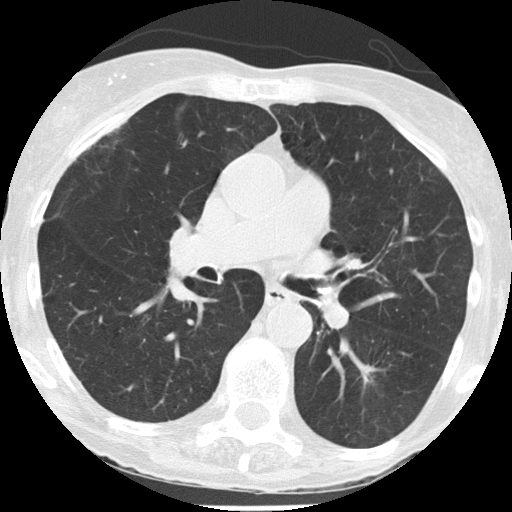
Axial slice from a low-dose chest CT screening exam; third screening round (two years after baseline); lung window (W 1500 / L -600 HU); slice 73 of 146 in the series; 512 × 512 image matrix, field of view 273 × 273 mm. Female, age 68 years at enrolment. Former smoker at enrolment.
Expert reader's lesion annotation, bounding box <339,350,397,401> (left, top, right, bottom; pixels). Reader record for this screening exam (exam-level; its link to the box is not recorded): non-calcified nodule or mass ≥4 mm, left lower lobe, 11 × 9 mm, spiculated (stellate) margins, soft tissue attenuation, pre-existing on the prior screen: yes; interval growth: yes. Official screen result: positive, other. Participant outcome: lung cancer diagnosed 164 days after this screen — non-small cell carcinoma, left lower lobe, poorly differentiated (G3), stage IA (AJCC 6th edition), 10 mm at pathology.